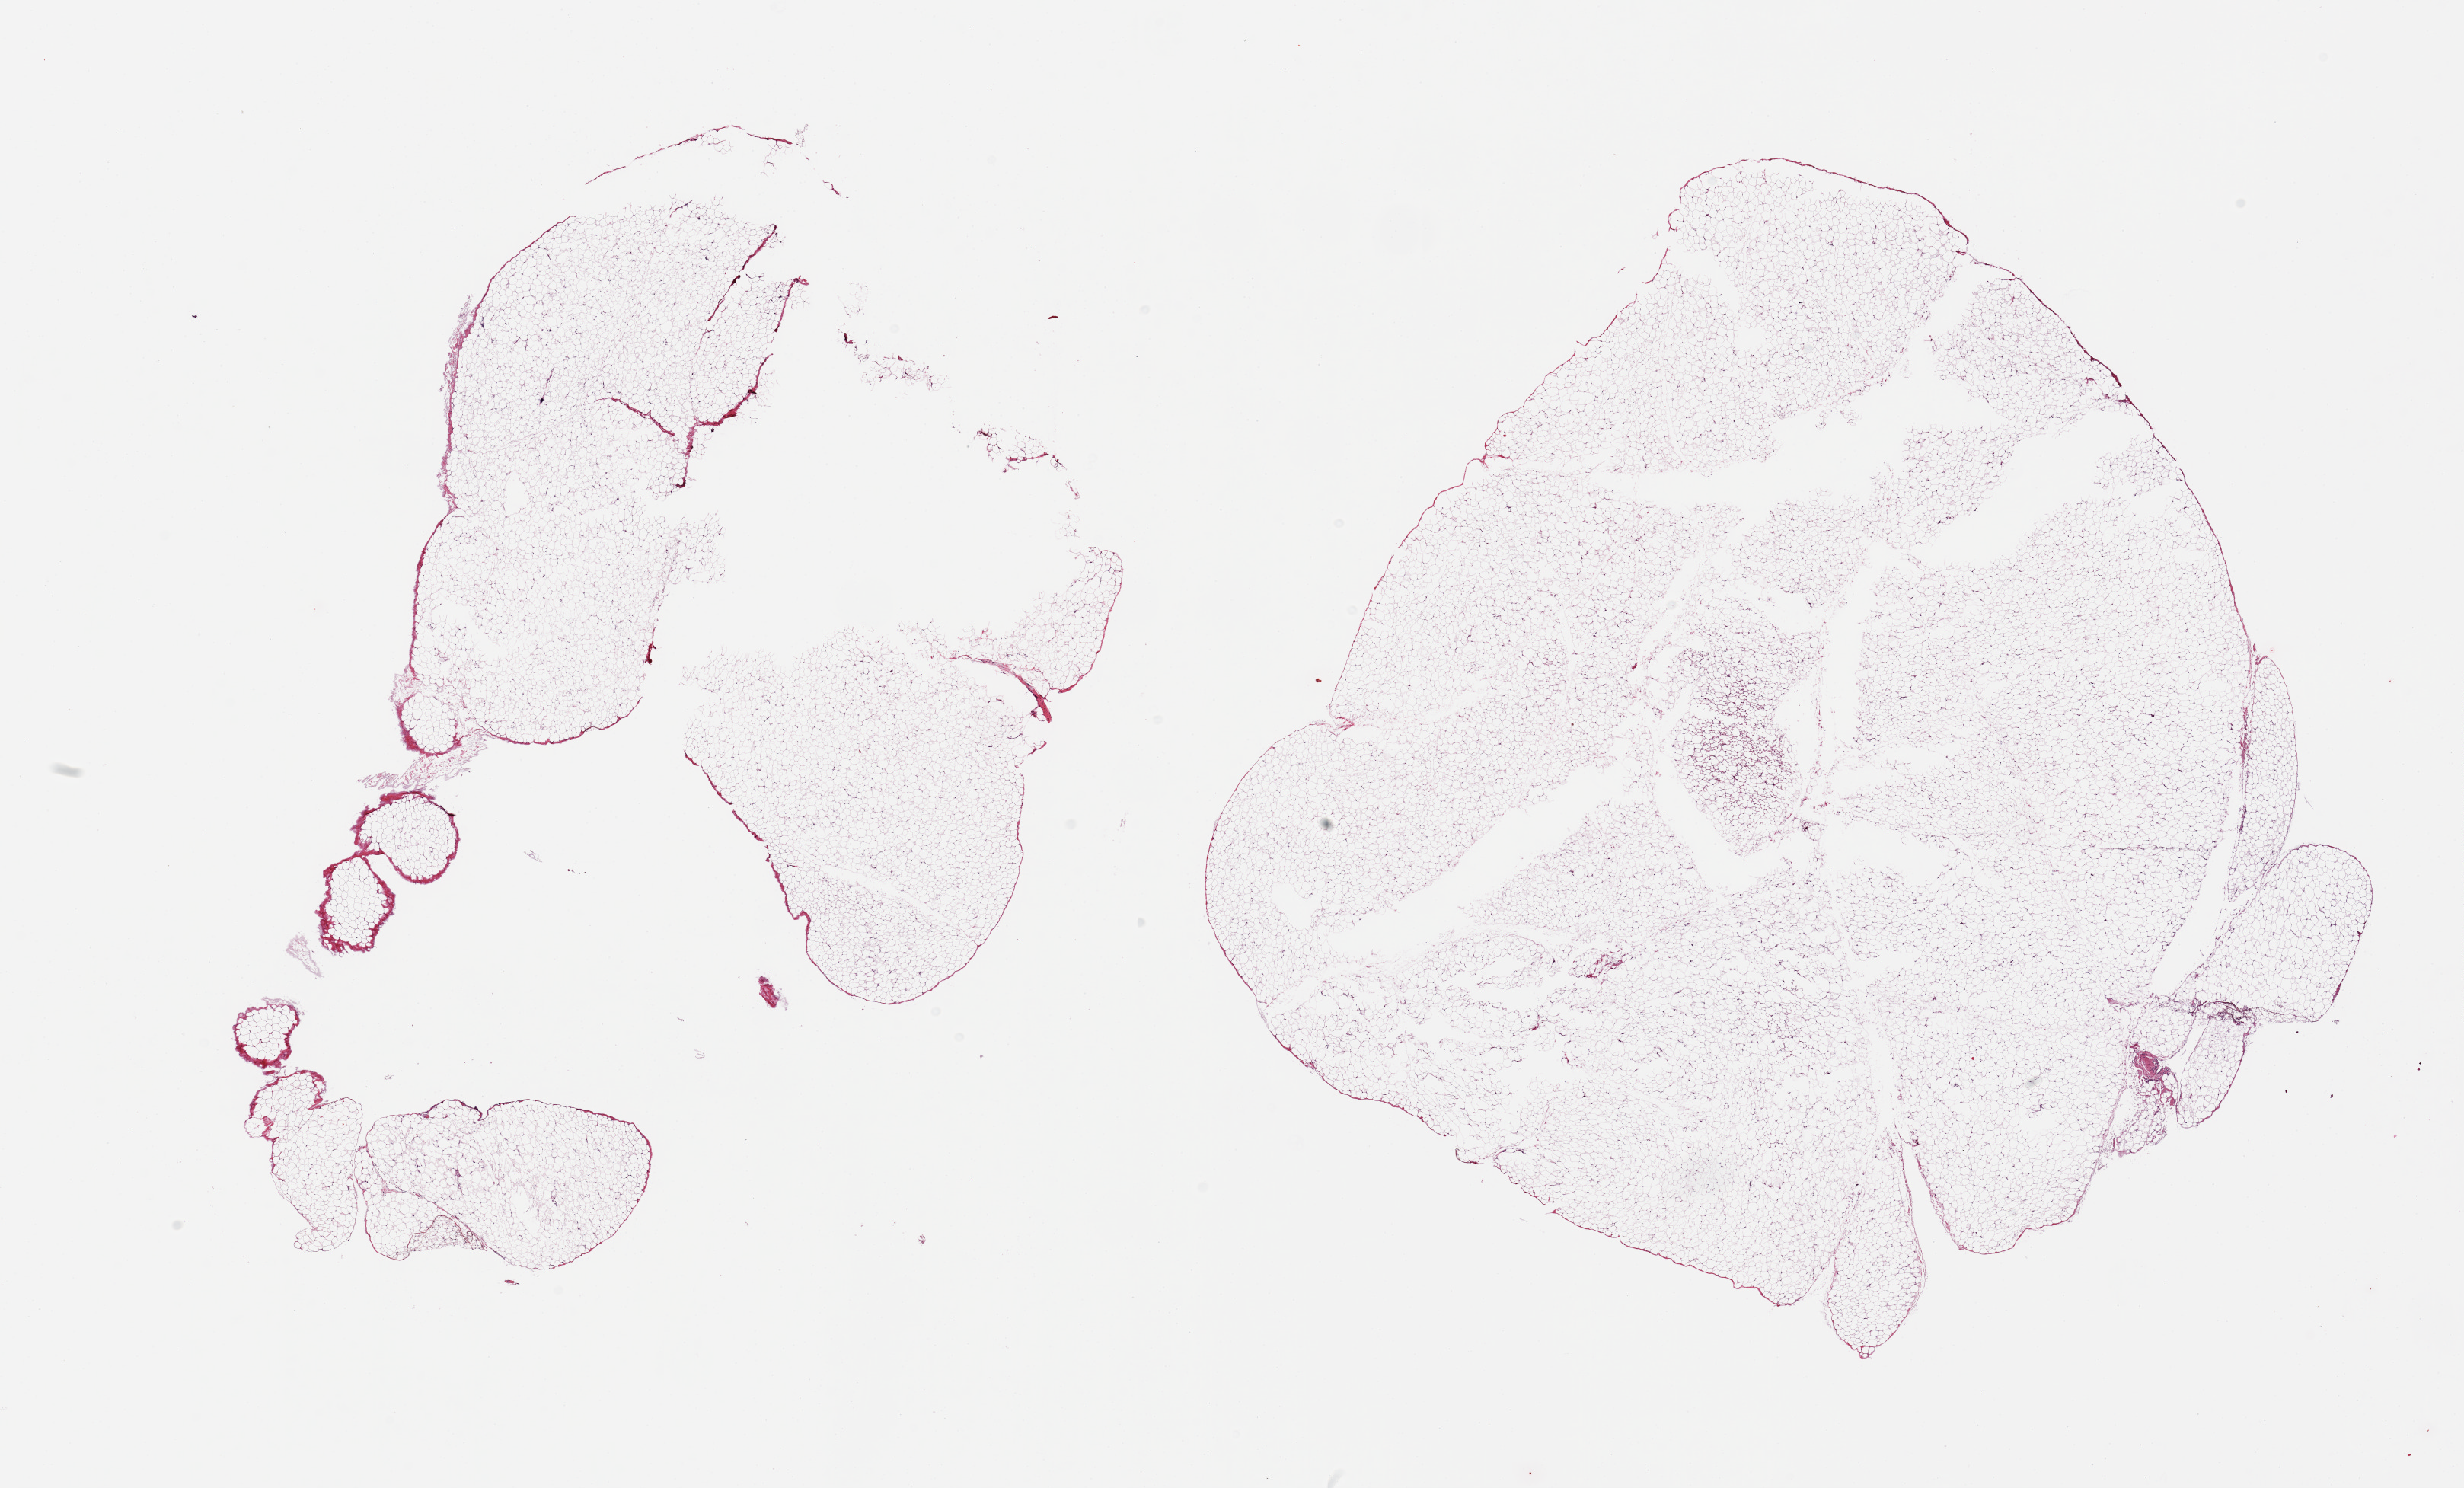
Digitized haematoxylin and eosin-stained section — a low-resolution overview of the entire scanned area, about 25.6 x 15.5 mm, PAXgene-fixed, paraffin-embedded tissue, sampled site (target tissue): omentum, tissue donor sample. Donor: female.
Pathologist's review note for this sample: 2 pieces, only trace fascia/vascular elements, good specimen.